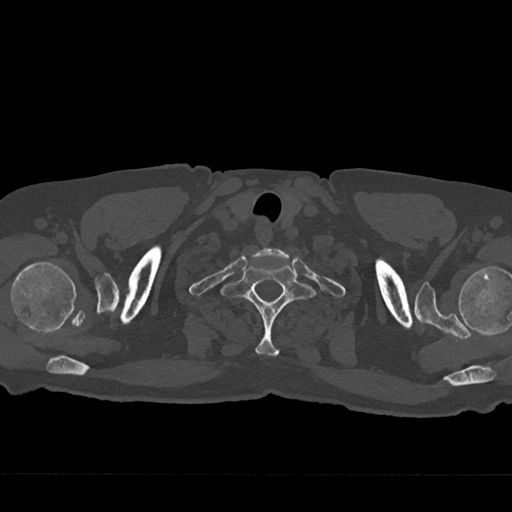
CT including the spine, one axial slice. Slice 661 of 797 in the series (ordered by position). Reconstruction kernel Br40s/3. 120 kVp. Bone window (W 1800 / L 400 HU). 0.5 mm slice thickness. 512 × 512 image matrix, field of view 377 × 377 mm. Male patient, age 75 years. Case-level facts recorded for this patient, not image findings: primary cancer: renal; vertebrae with lytic lesions (as recorded): T4.
Structures marked on this image (semi-automatically segmented with operator editing):
- T1 vertebra: box from (x=220, y=265) to (x=320, y=356) px
- T2 vertebra: (x=280, y=293)–(x=283, y=296)